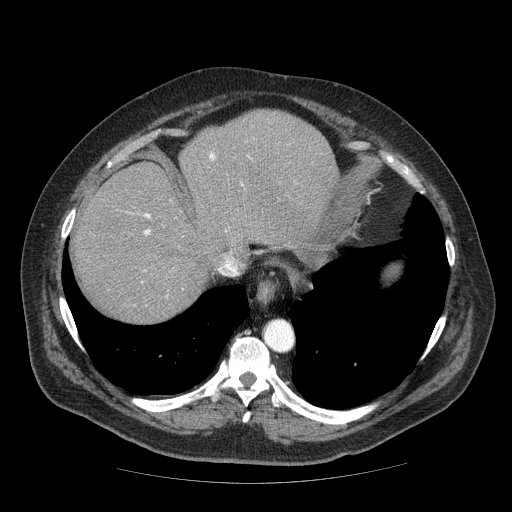
Contrast-enhanced abdominal CT (liver protocol), one axial slice. Slice 57 of 85 in the series (ordered by position). Reconstruction kernel STANDARD. 120 kVp. Soft-tissue window (W 400 / L 40 HU). 2.5 mm slice thickness. 512 × 512 image matrix. From the clinical record (not read from this slice): diagnosis: hepatocellular carcinoma (patient treated with transarterial chemoembolisation; whether this scan precedes or follows treatment is not stated here); TNM stage (as recorded): Stage-IIIA; Child-Pugh class: A; tumour nodularity: multinodular.
Structures marked on this image (semi-automatically segmented with operator editing):
- abdominal aorta: bounding box <265,321,294,351> (left, top, right, bottom; pixels)
- liver parenchyma outside the tumour (the mass and vessels are separate outlines, so this box may not span the whole liver): <74,110,338,322>
- liver vessels: <144,153,215,235>